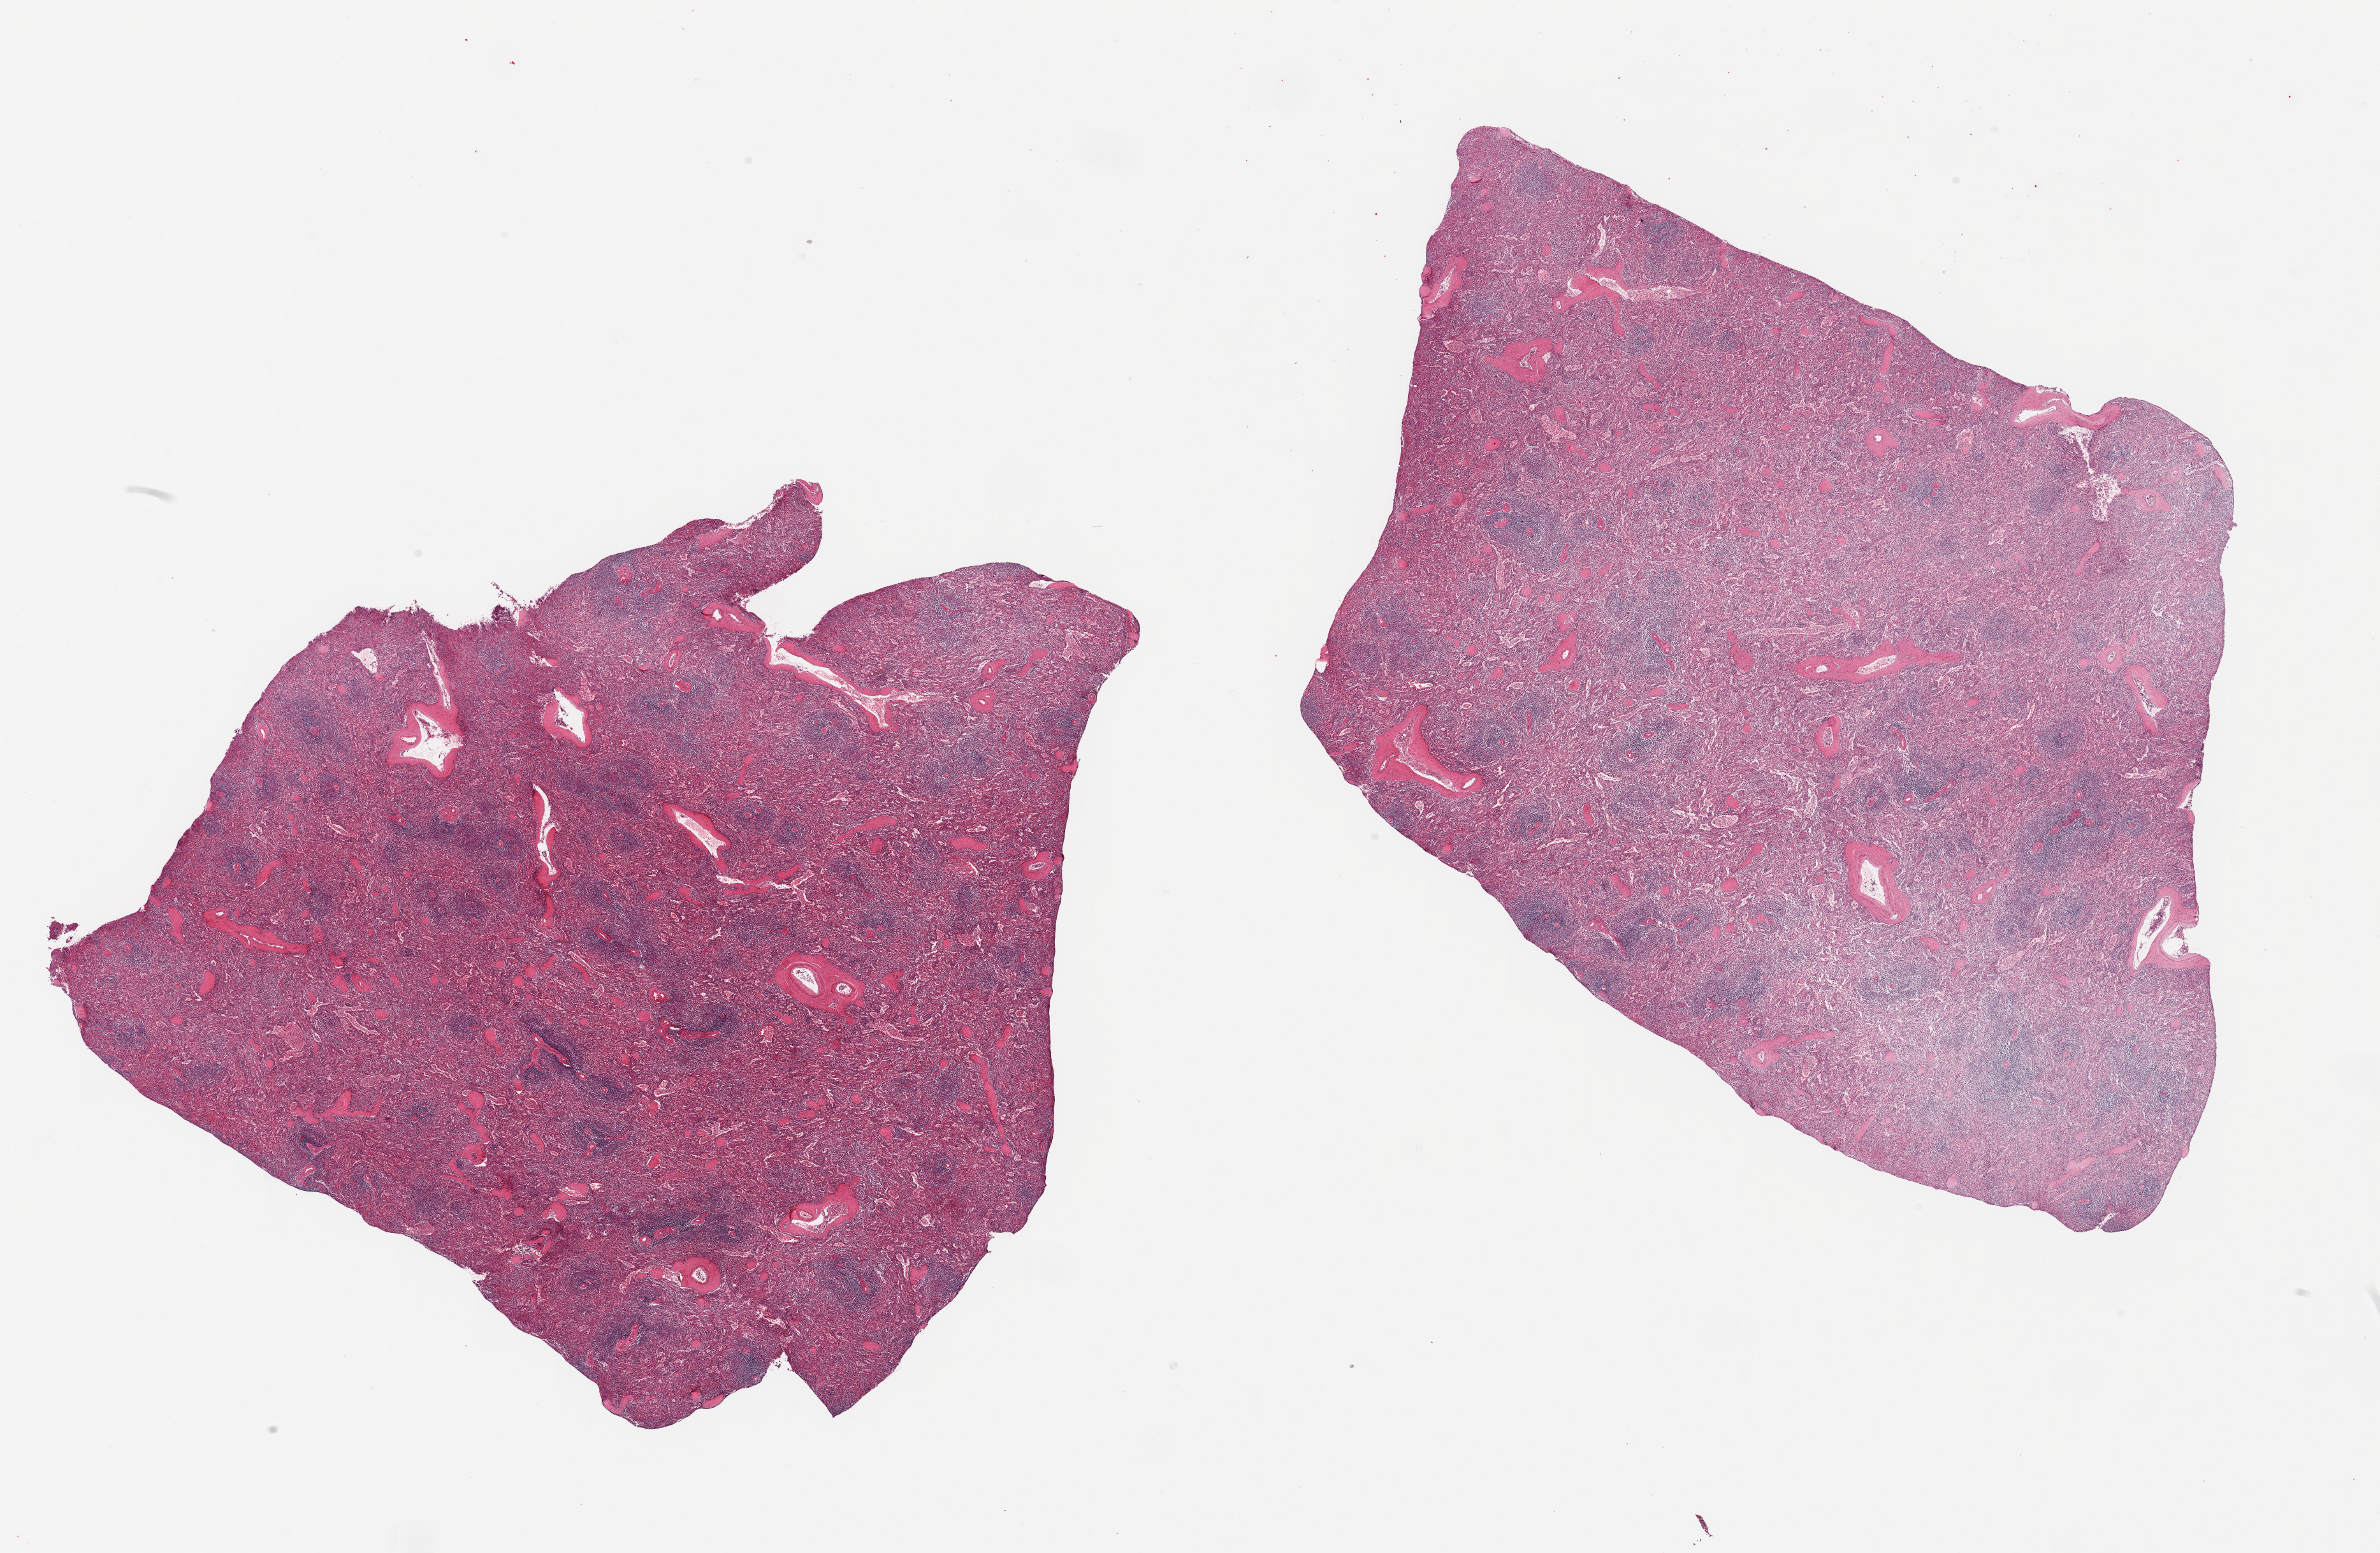
Digitized H&E-stained section — a low-resolution overview of the entire scanned area, about 29.5 x 19.3 mm. PAXgene-fixed, paraffin-embedded tissue. Target tissue: spleen. Tissue donor sample. Donor sex: male.
- reviewer comment on this tissue sample: 2 pieces, no abnormalities